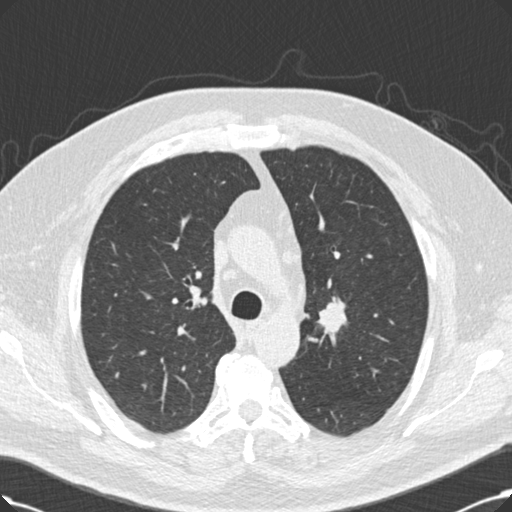
Axial slice from a low-dose chest CT screening exam, third screening round (two years after baseline), lung window (W 1500 / L -600 HU), standard (soft-tissue) reconstruction kernel (B30f). Male, age 60 years at enrolment. Current smoker at enrolment.
Lesion marked by an expert reader, bounding box (x1, y1, x2, y2) in pixels: (318, 296, 349, 330). The exam's reader record, not a measurement of the box and not confirmed to be the same lesion: non-calcified nodule or mass ≥4 mm, left upper lobe, 20 × 20 mm, smooth margins, soft tissue attenuation, pre-existing on the prior screen: no. Official screen result: positive, other. Lung cancer was diagnosed 53 days after this screen: squamous cell carcinoma, NOS, right upper lobe, 27 mm at pathology.